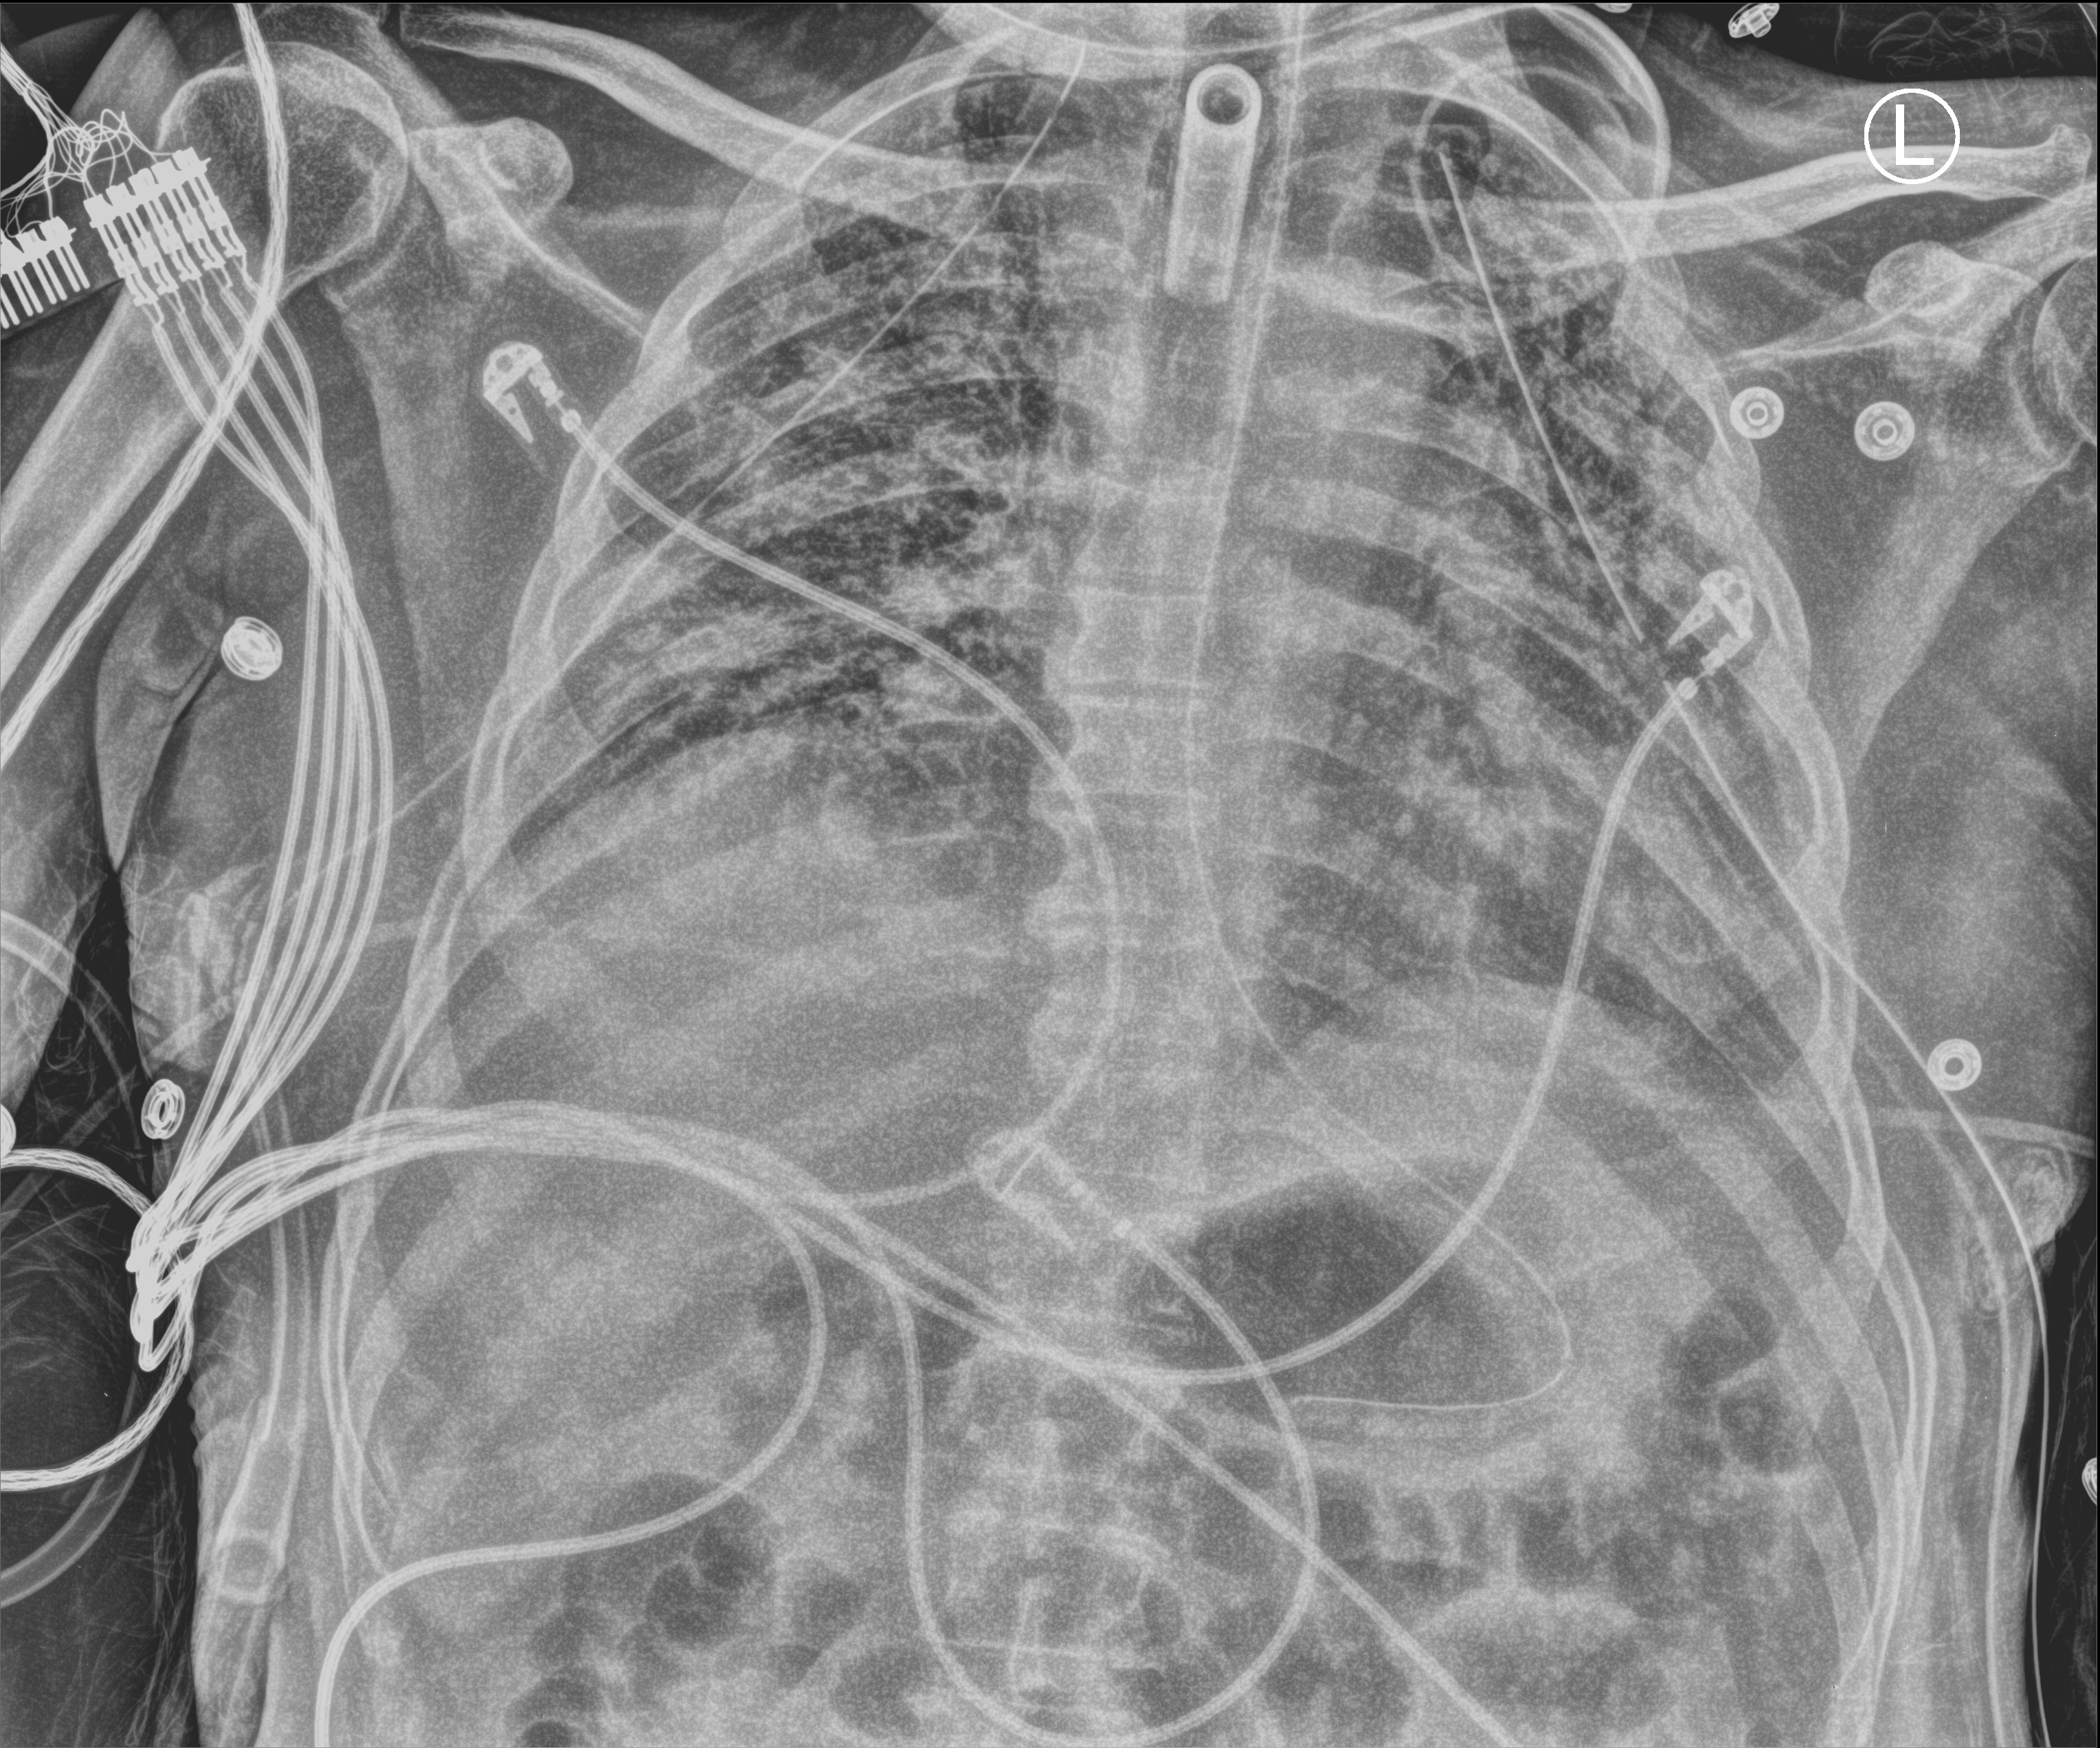
Bedside chest radiograph (computed radiography); anteroposterior (AP) projection. Patient hospitalised with COVID-19; male, aged 18–59 years.
Admission-level facts for this patient (not findings on this image; timing relative to this image not recorded):
- length of hospital stay: 83 days
- mechanically ventilated during this hospital stay: yes
- admitted to intensive care during this hospital stay: yes